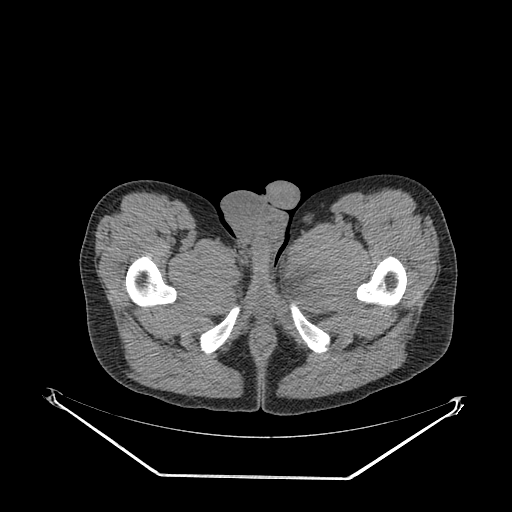
CT of an extremity soft-tissue mass (from a PET/CT study), one axial slice. Position 44 of 267 along the scan axis. Reconstruction kernel SOFT. Soft-tissue window (W 400 / L 40 HU). 3.75 mm slice thickness. 512 × 512 image matrix, field of view 500 × 500 mm. Male patient. From the clinical record (not read from this slice): histological type: pleiomorphic liposarcoma; grade: high; site of the primary tumour: left thigh.
Structures marked on this image (expert contour drawn on MRI and transferred to this co-registered scan by the dataset authors):
- gross tumour volume including surrounding oedema: bounding box <288,265,343,316> (left, top, right, bottom; pixels)